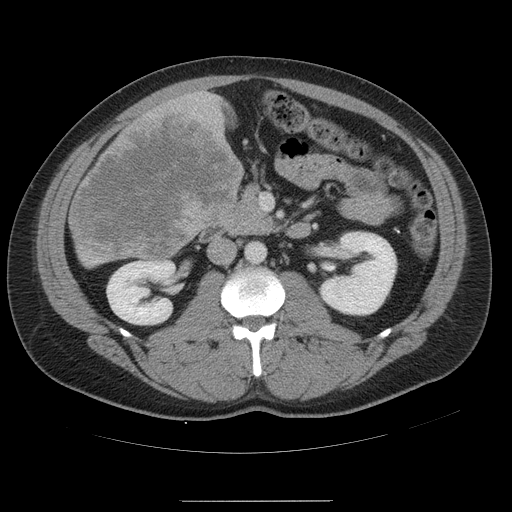
Contrast-enhanced abdominal CT, one axial slice; slice 19 of 54 in the series (ordered by position); 120 kVp; intravenous contrast given; soft-tissue window (W 400 / L 40 HU); 5 mm slice thickness; 512 × 512 image matrix. Male patient, age 40 years. From the clinical record (not read from this slice): diagnosis: colorectal cancer liver metastases, imaged before liver resection; multiple liver metastases: no.
Outlined on this slice (manually delineated by an expert):
- liver: bounding box (x1, y1, x2, y2) in pixels: (69, 91, 244, 267)
- liver metastasis: (71, 109, 242, 259)